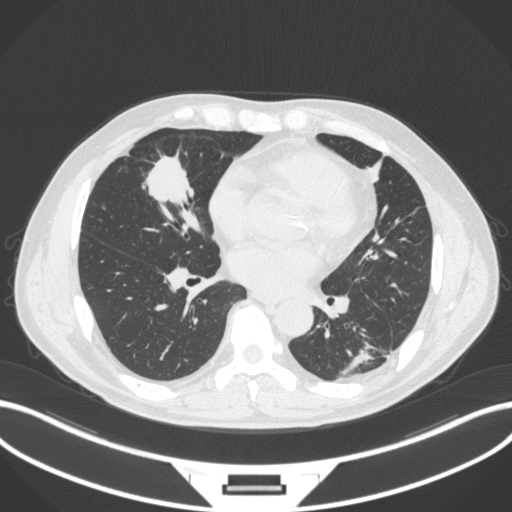
Chest CT, one axial slice; reconstruction kernel B31f; lung window (W 1500 / L -600 HU); 1 mm slice thickness; 512 × 512 image matrix. Male patient, age 59 years. Case-level facts recorded for this patient, not image findings: clinical TNM (as recorded): T2a N1 M0.
Structures marked on this image (bounding box drawn by a radiologist):
- lung tumour (recorded histology: adenocarcinoma): bounding box <142,153,198,208> (left, top, right, bottom; pixels)